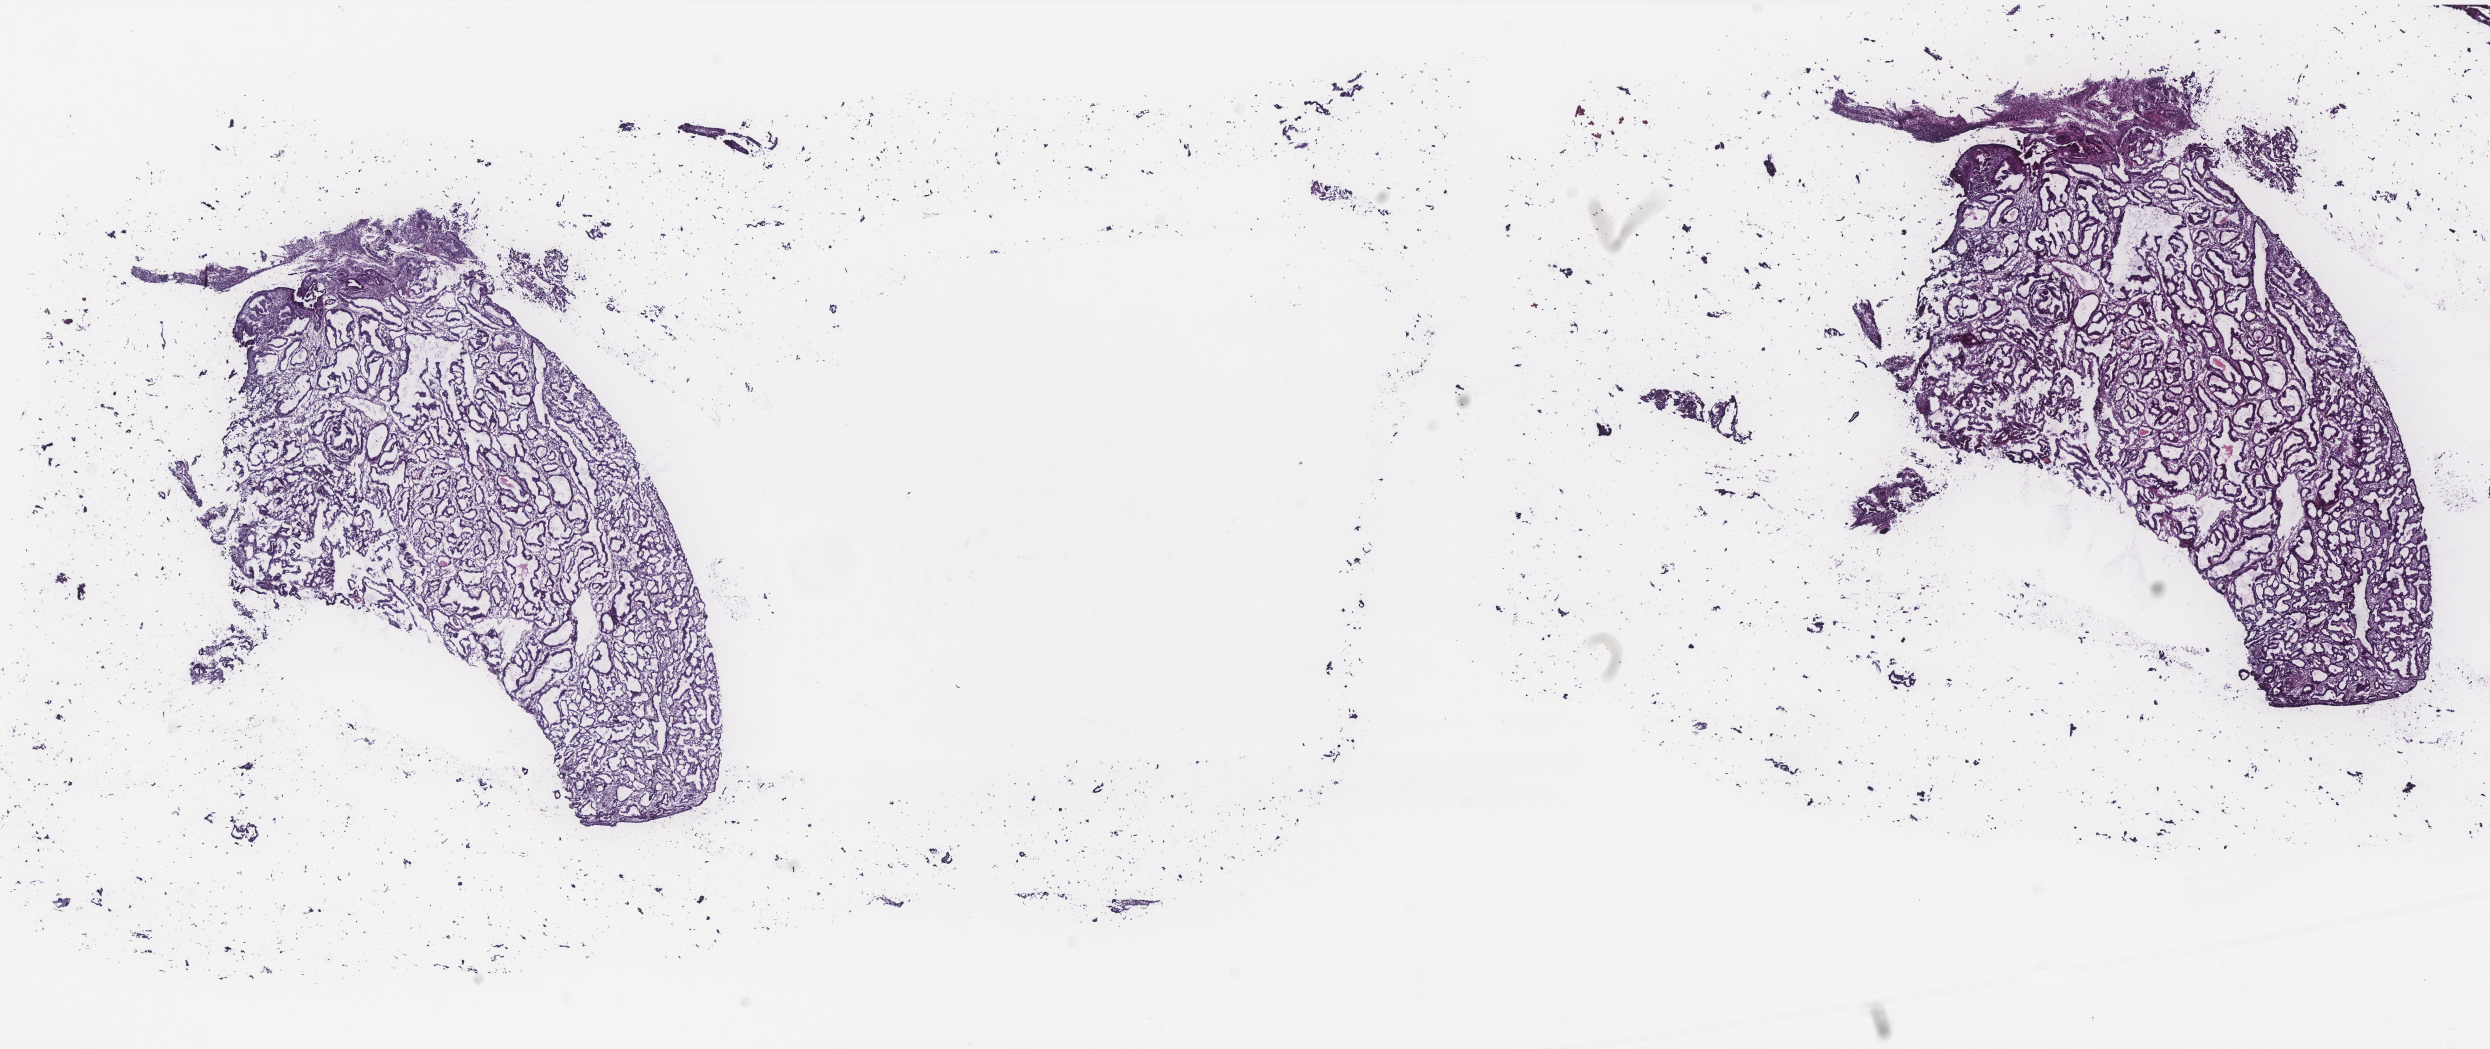
Whole-slide histology image, Hematoxylin and eosin (H&E) stained — shown as a low-resolution overview of the whole scanned area (about 20.0 x 8.4 mm, acquisition: 40x scan). Frozen section. Uterus, primary tumour sample. Female patient; age at initial diagnosis 67 years. Histologic grade: G1 (well differentiated). Pathologist review of this section (percent, as recorded): tumour cells 100%, tumour nuclei 65%, normal cells 0%, stromal cells 0%, necrosis 0%. Infiltration values recorded for this section: lymphocyte infiltration 0%, monocyte infiltration 0%, neutrophil infiltration 0%.
FIGO stage: IA. Pathologic diagnosis: Endometrioid adenocarcinoma, NOS.